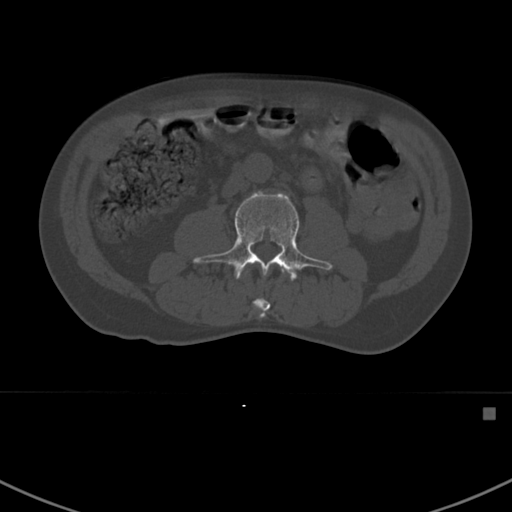
CT including the spine, one axial slice. Slice 266 of 412 in the series (ordered by position). Reconstruction kernel Br40s. Bone window (W 1800 / L 400 HU). 1.5 mm slice thickness. 512 × 512 image matrix. Male patient, age 59 years. Case-level facts recorded for this patient, not image findings: primary cancer: prostate.
Structures marked on this image (semi-automatic segmentation, software-assisted and operator-edited):
- L2 vertebra: bounding box (x1, y1, x2, y2) in pixels: (246, 269, 286, 318)
- L3 vertebra: (192, 191, 333, 282)